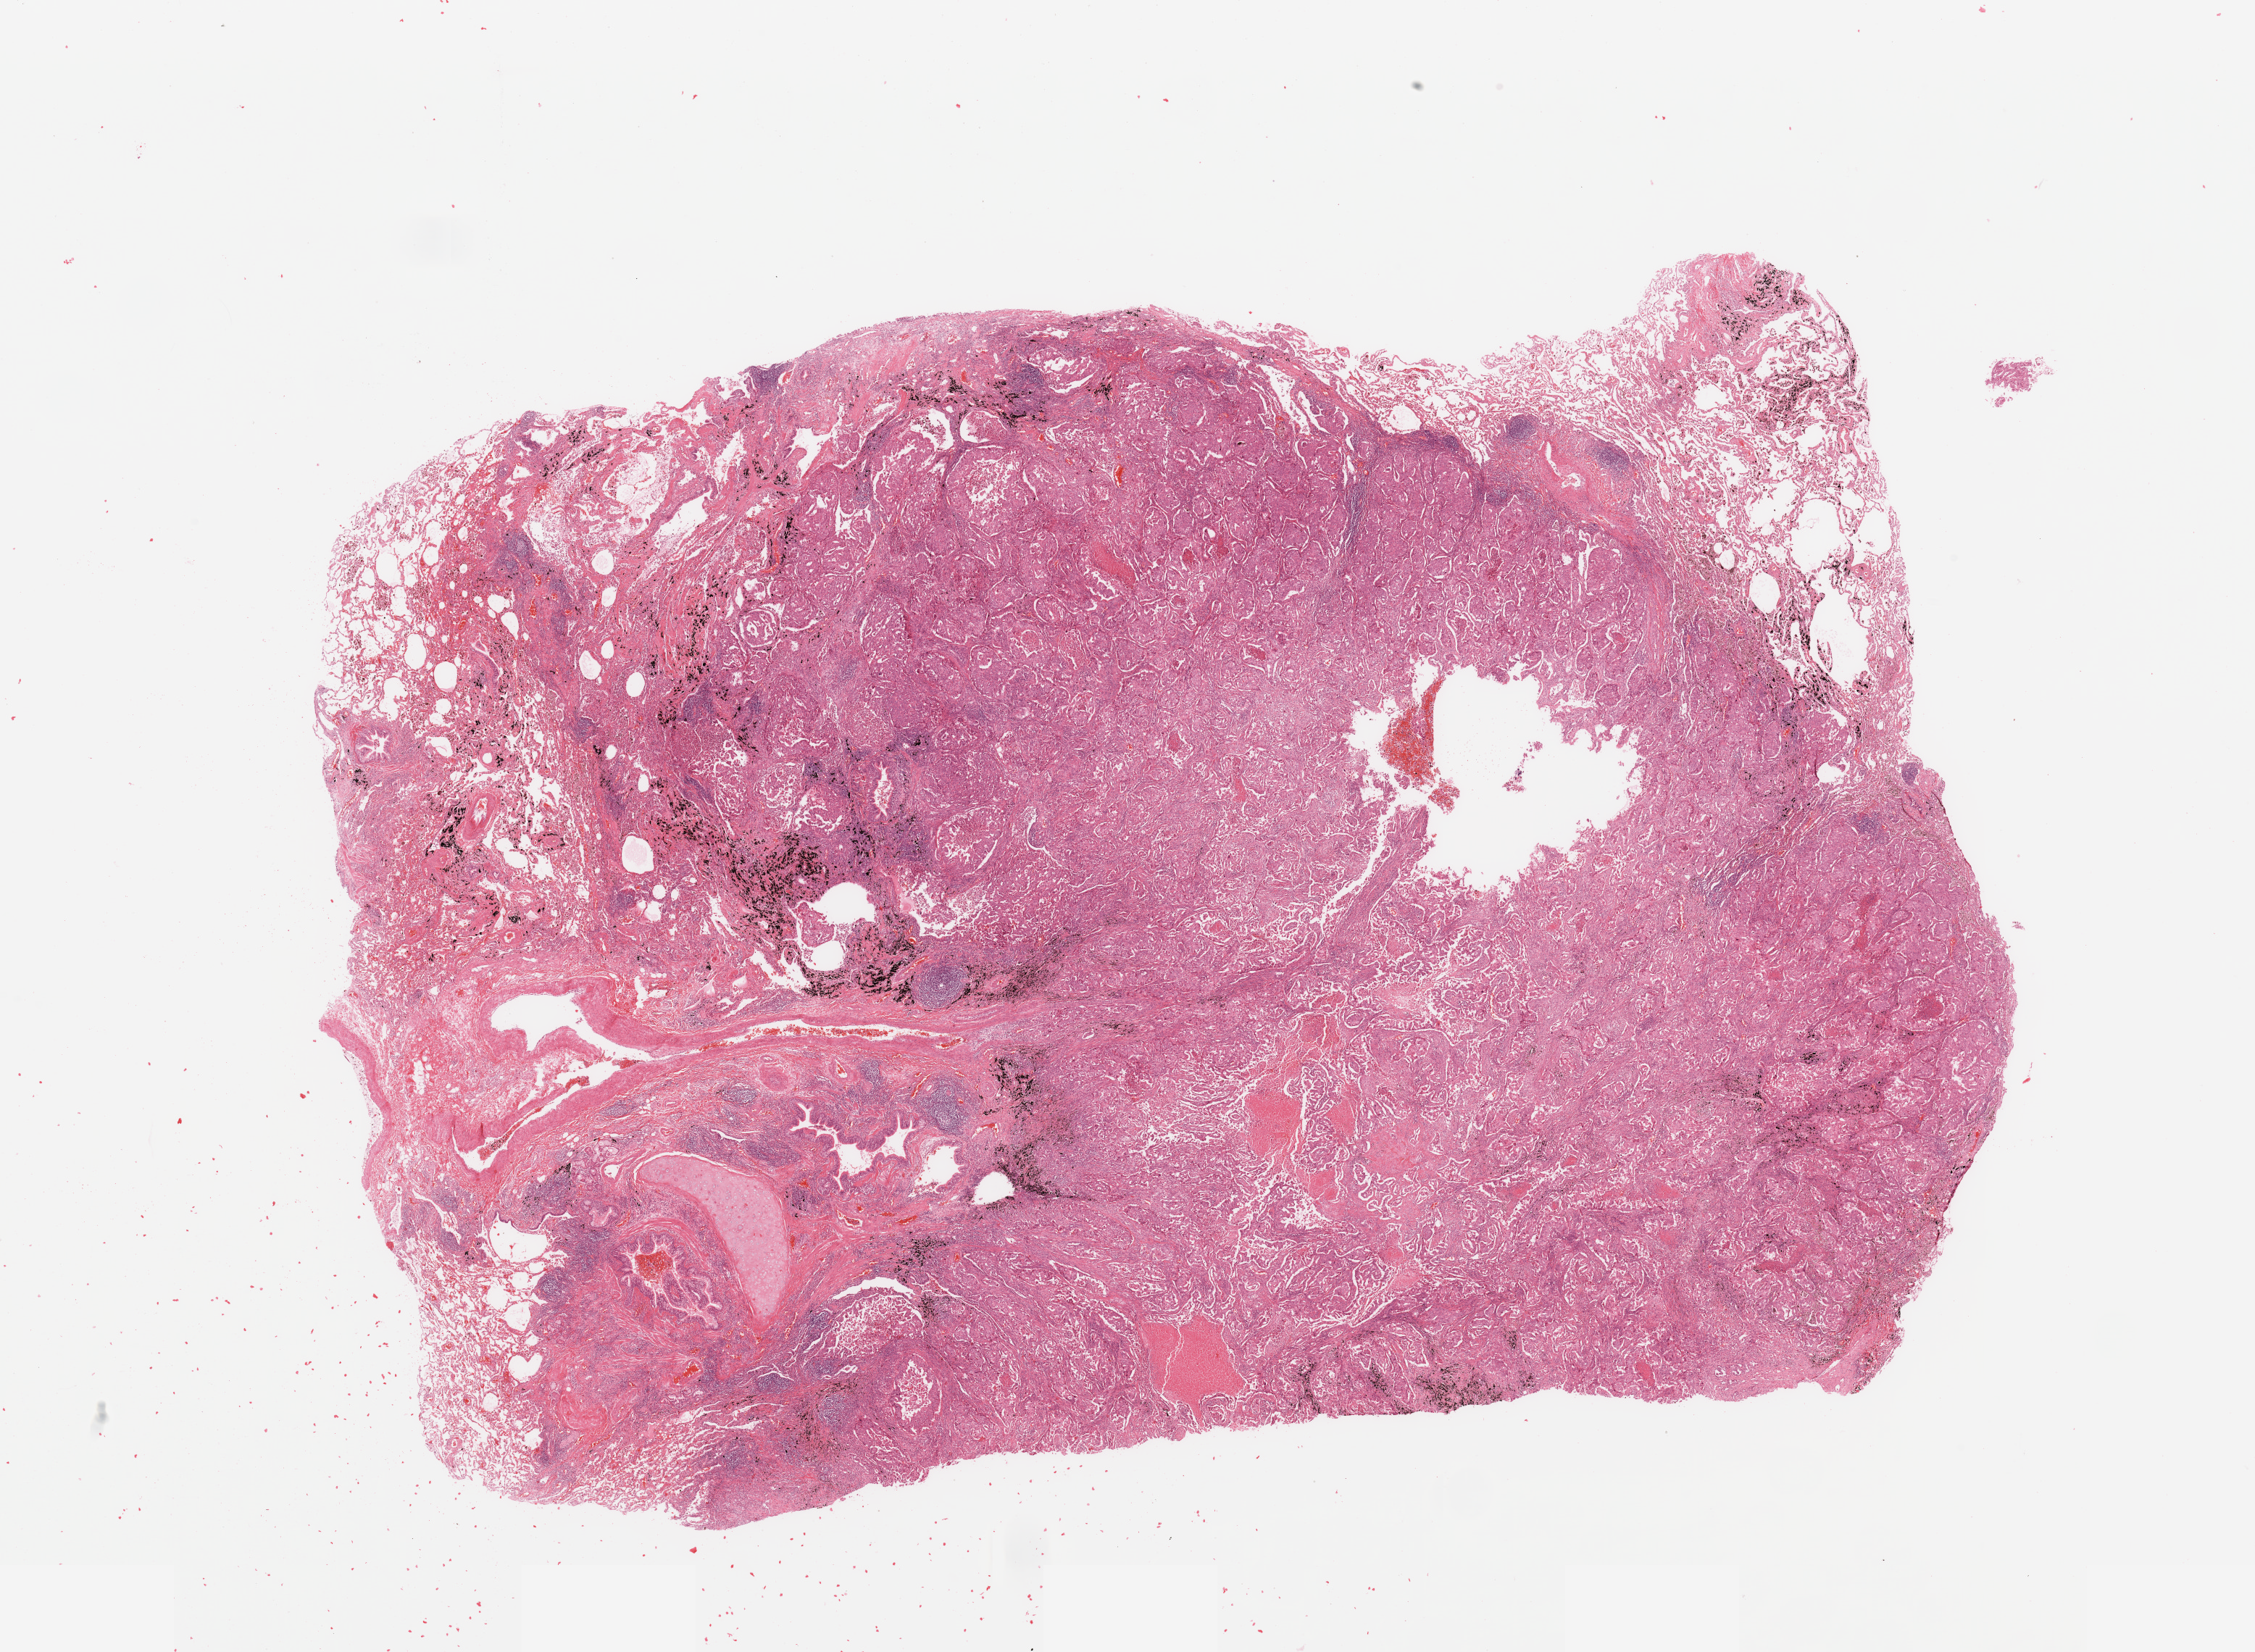
Hematoxylin and eosin (H&E) stained whole-slide image — shown as a low-resolution overview of the whole scanned area (about 24.6 x 18.0 mm), tumour tissue sample, lung. Male, 56 y/o. Histologic grade: G3 (poorly differentiated).
- AJCC pathologic stage: IB
- primary tumour site (as recorded): right upper lobe
- histologic diagnosis: Adenocarcinoma, NOS